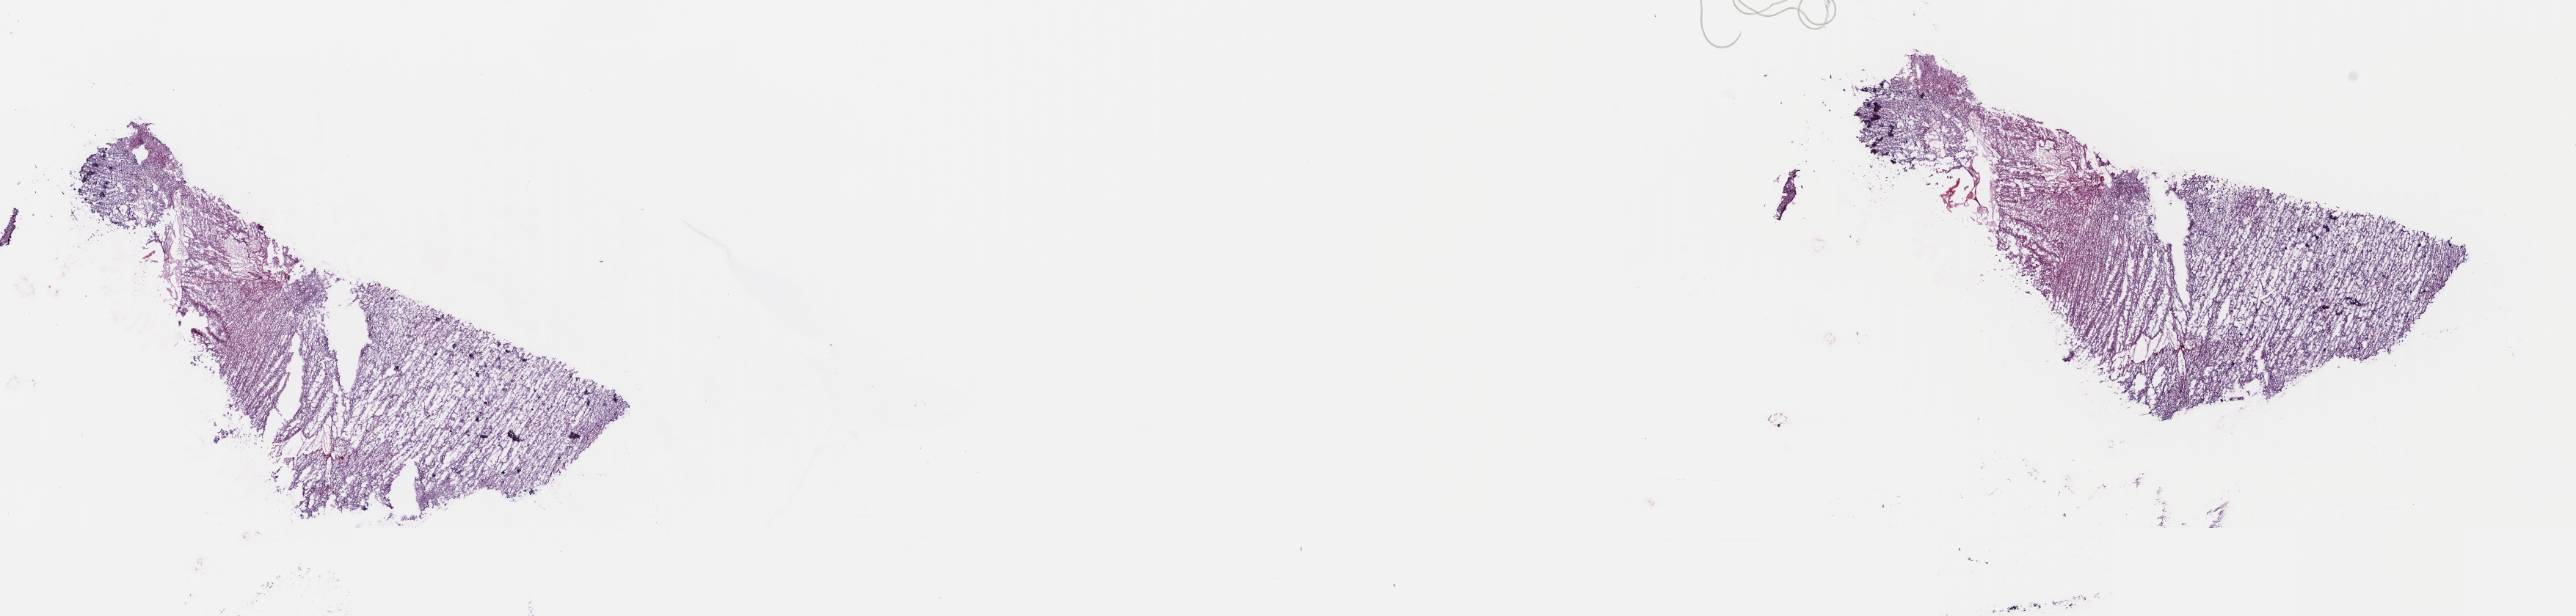
H&E-stained whole-slide image, whole scanned area (about 27.6 x 6.6 mm) shown as a low-resolution overview, frozen section, primary tumour sample from the brain. Female patient; age at initial diagnosis 55 years. Histologic grade: G3 (poorly differentiated). Composition of this section per pathologist review: tumour cells 50%, tumour nuclei 90%, normal cells 10%, stromal cells 40%, necrosis 0%. Infiltration values recorded for this section: lymphocyte infiltration 0%, monocyte infiltration 0%, neutrophil infiltration 0%.
Pathologic diagnosis: Mixed glioma (cerebrum).